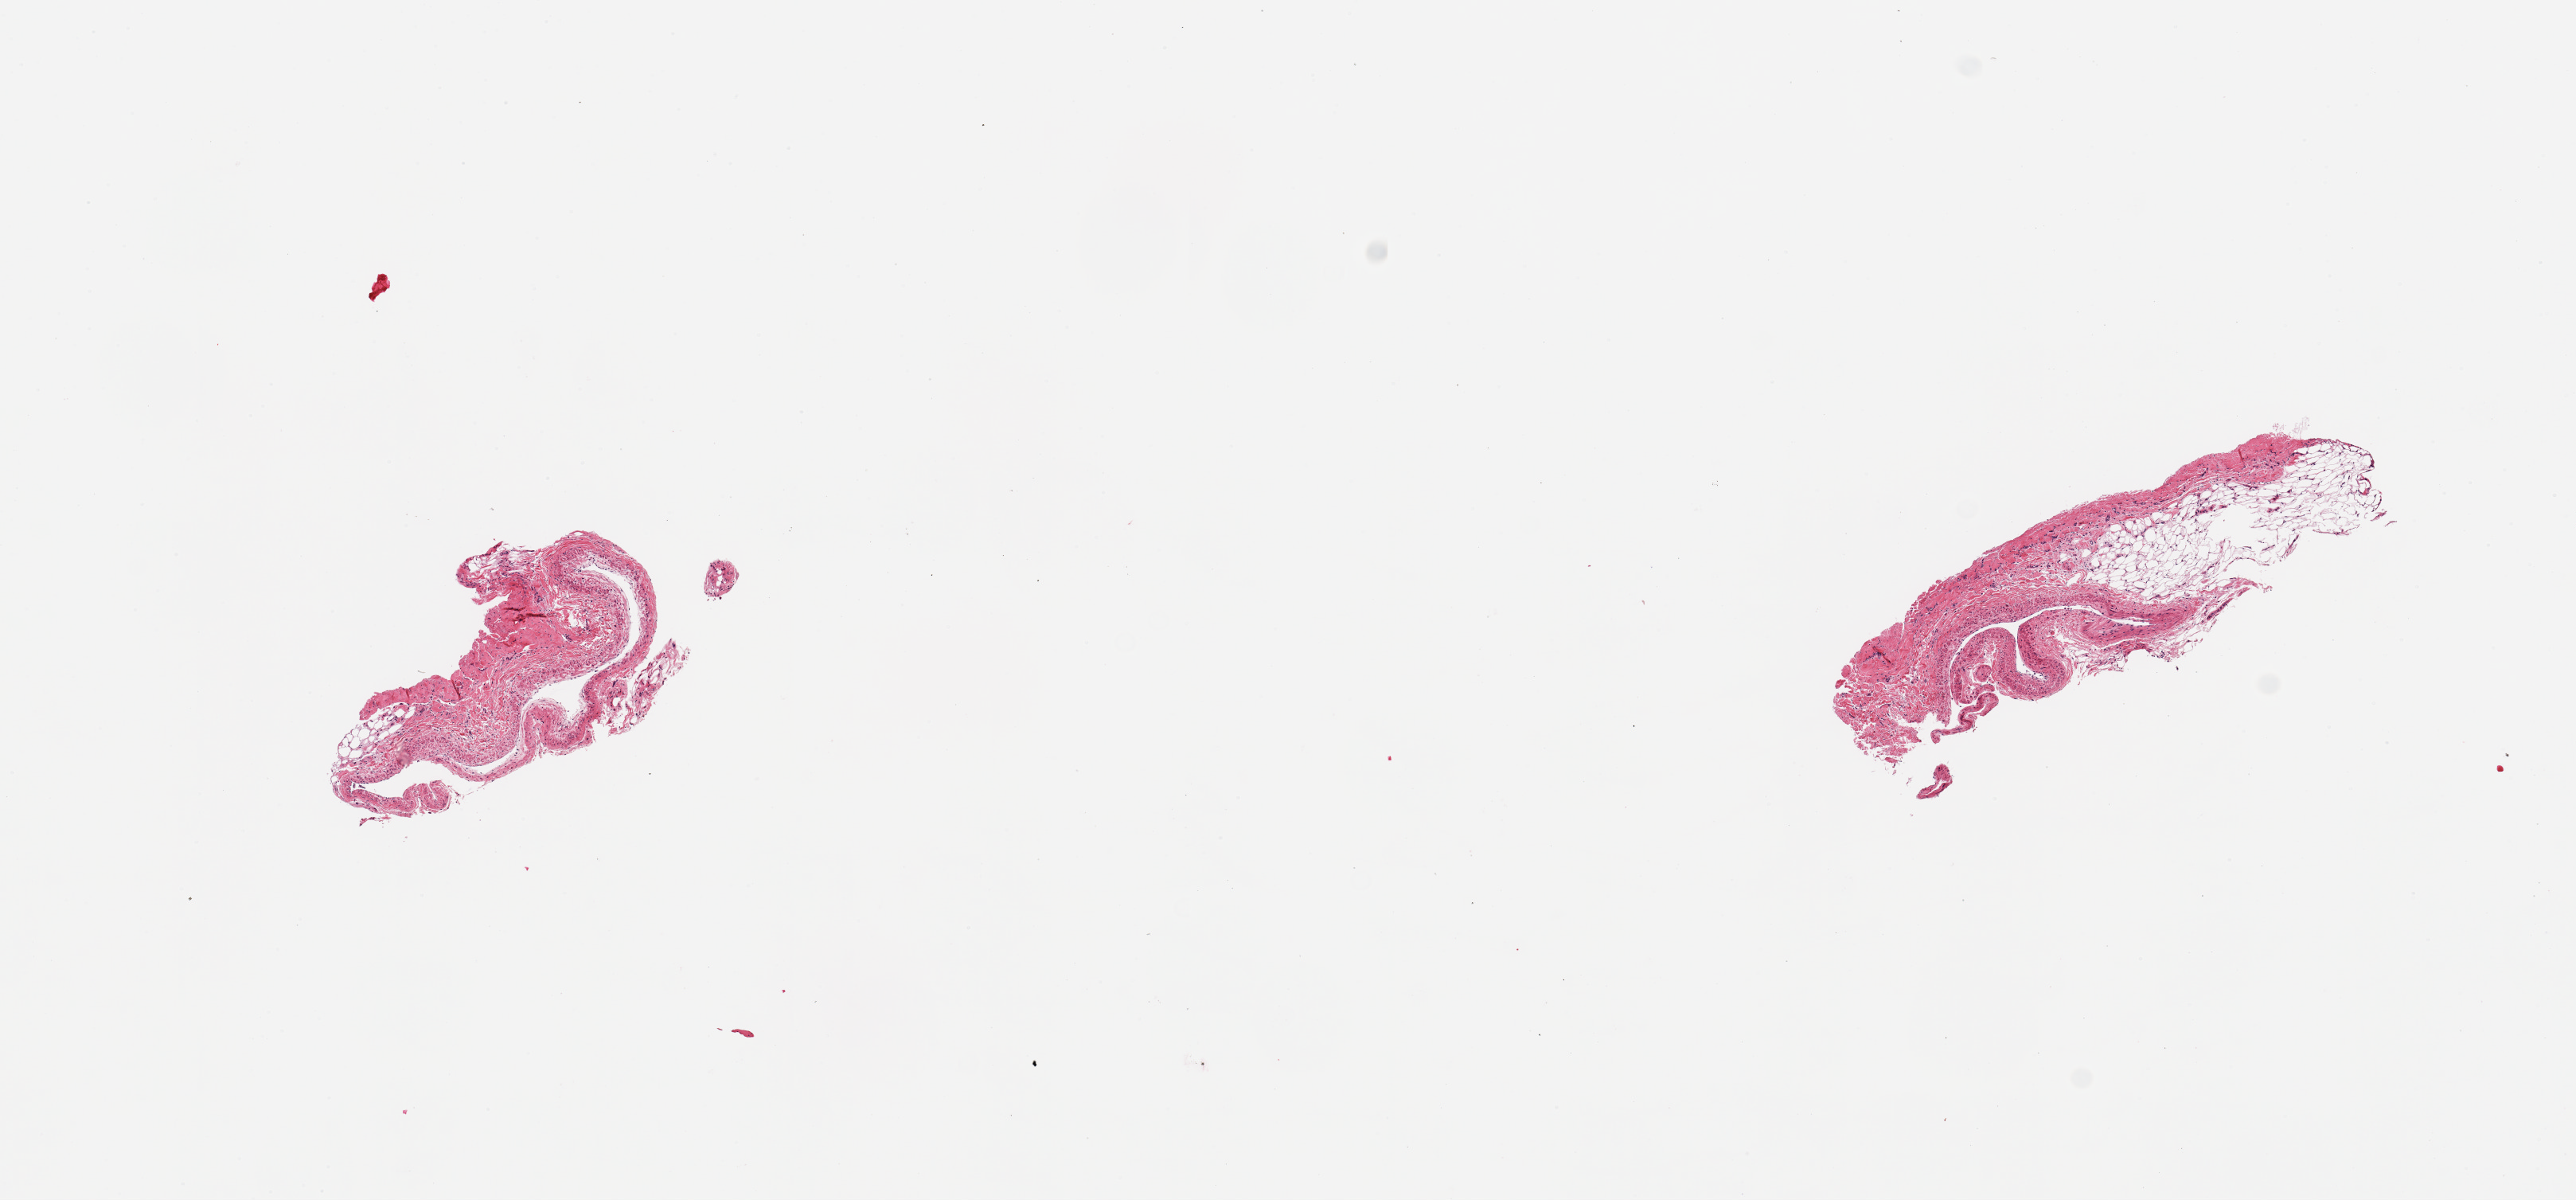
Digitized hematoxylin and eosin (H&E)-stained section, brightfield — whole scanned area (about 12.8 x 6.0 mm) shown as a low-resolution overview; PAXgene-fixed, paraffin-embedded tissue; target tissue: coronary artery; tissue donor sample. Donor: male.
Reviewer comment on this tissue sample: 2 pieces; vein not artery; history of coronary artery bypass grafts.